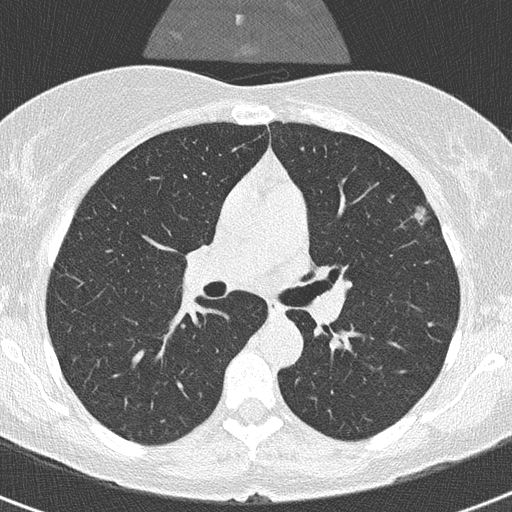
Low-dose screening chest CT, axial slice. Second screening round (one year after baseline). Lung window (W 1500 / L -600 HU). 2 mm slice thickness. Lung (sharp) reconstruction kernel (B50f). Slice 119 of 320 in the series. 512 × 512 image matrix. Female participant, aged 56 years at enrolment. Former smoker at enrolment.
Expert reader's lesion annotation, bounding box <407,201,456,254> (left, top, right, bottom; pixels). Screening reader's record for this exam (one nodule recorded; not confirmed to be the boxed lesion): non-calcified nodule or mass ≥4 mm, left upper lobe, 20 × 9 mm, smooth margins, soft tissue attenuation, pre-existing on the prior screen: yes; interval growth: yes. Later outcome: lung cancer diagnosed 55 days after this screen — adenocarcinoma, NOS, left upper lobe, moderately differentiated (G2), stage IA (AJCC 6th edition), 11 mm at pathology.